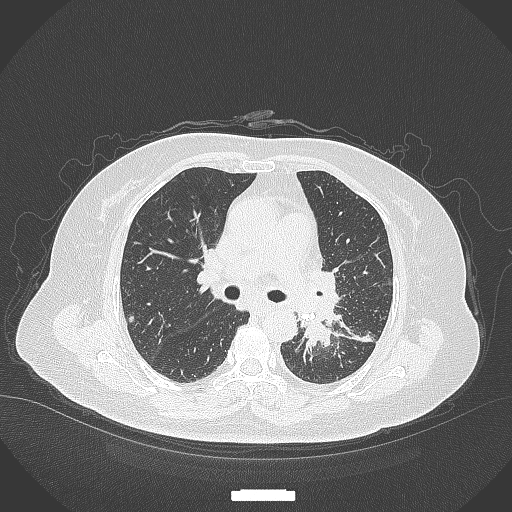
Chest CT, one axial slice. Position 211 of 322 along the scan axis. 120 kVp. Lung window (W 1500 / L -600 HU). 1 mm slice thickness. 512 × 512 image matrix, field of view 400 × 400 mm. Female patient, age 69 years. From the clinical record (not read from this slice): clinical TNM (as recorded): T2b N3 M1.
Structures marked on this image (rectangle marked by the reading radiologist):
- lung tumour (recorded histology: adenocarcinoma): bounding box [x1, y1, x2, y2] px = [298, 307, 336, 364]